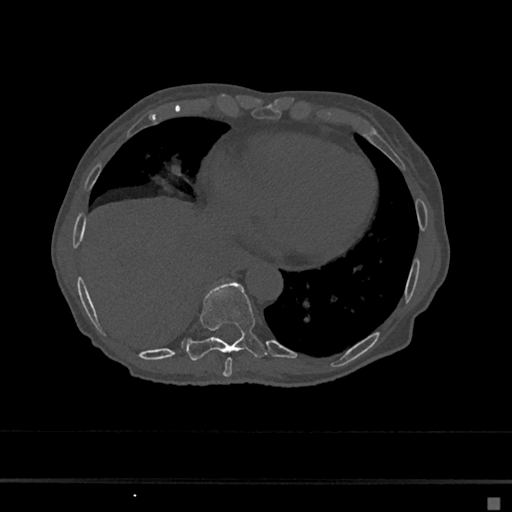
CT including the spine, one axial slice; slice 277 of 797 in the series (ordered by position); 120 kVp; bone window (W 1800 / L 400 HU); 512 × 512 image matrix, field of view 360 × 360 mm. Female patient, age 68 years. From the clinical record (not read from this slice): primary cancer: renal.
Annotated regions visible in this slice (semi-automatic segmentation, software-assisted and operator-edited):
- T8 vertebra: bounding box <223,357,232,377> (left, top, right, bottom; pixels)
- T9 vertebra: <187,282,266,361>